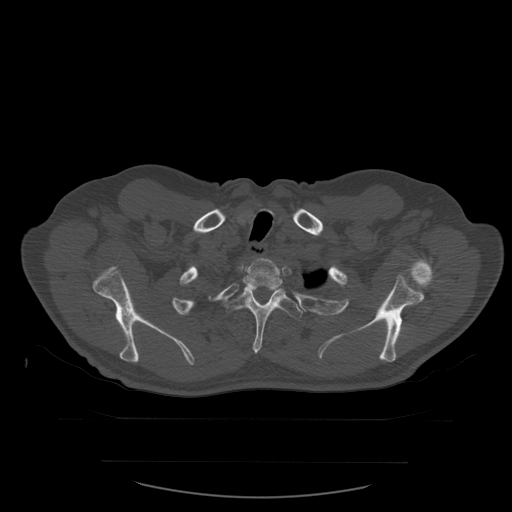
CT including the spine, one axial slice; slice 465 of 590 in the series (ordered by position); bone window (W 1800 / L 400 HU); 512 × 512 image matrix. Patient age 71 years. From the clinical record (not read from this slice): primary cancer: lung; vertebrae with lytic lesions (as recorded): T1, T2, L5, S1.
Annotated regions visible in this slice (semi-automatic segmentation, software-assisted and operator-edited):
- T2 vertebra: bounding box [x1, y1, x2, y2] px = [243, 258, 284, 290]
- T3 vertebra: [224, 288, 303, 354]